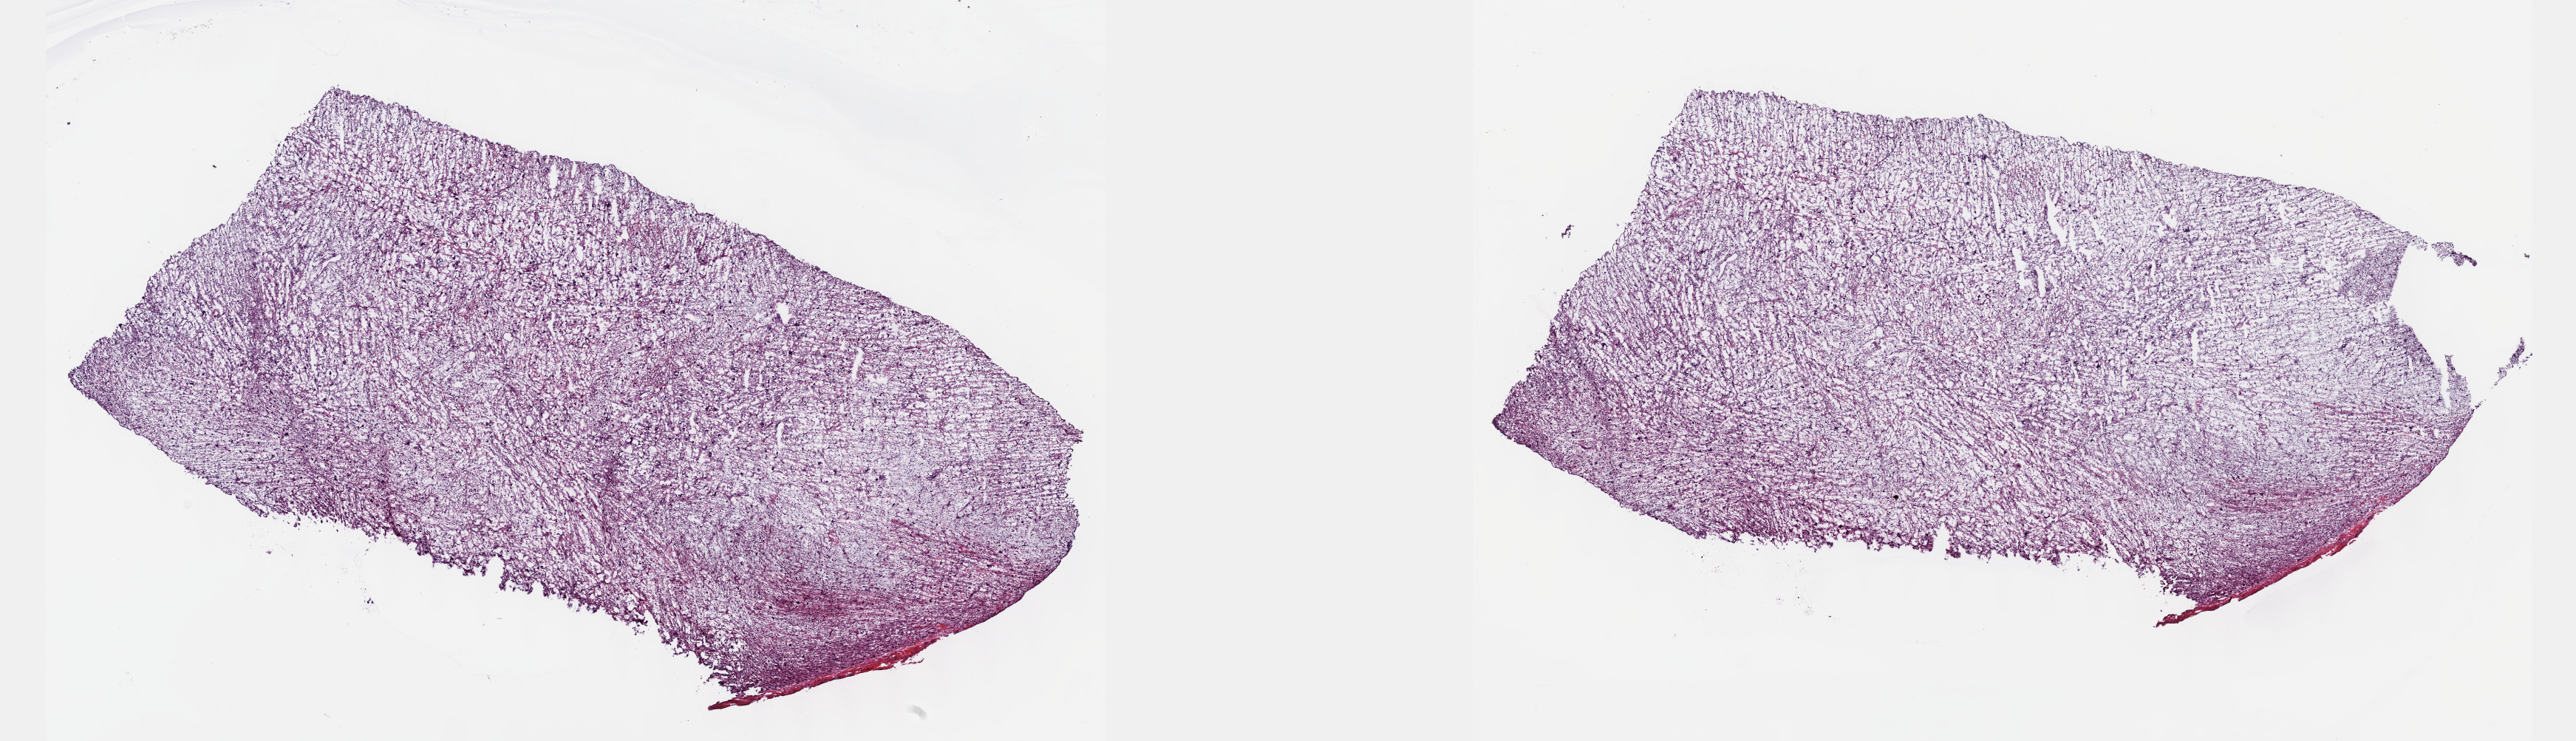
Whole-slide histology image, H&E, low-resolution overview of the scanned area, about 28.2 x 8.1 mm (from a 40x scan). Frozen section from the top of the tissue portion. Primary tumour sample from the connective, subcutaneous and other soft tissues. Male patient; age at initial diagnosis 49 years. Composition of this section per pathologist review: tumour cells 100%, tumour nuclei 75%, normal cells 0%, stromal cells 0%, necrosis 0%. Infiltration values recorded for this section: lymphocyte infiltration 3%, monocyte infiltration 0%, neutrophil infiltration 0%.
Histologic diagnosis: Undifferentiated sarcoma (connective, subcutaneous and other soft tissues of lower limb and hip).